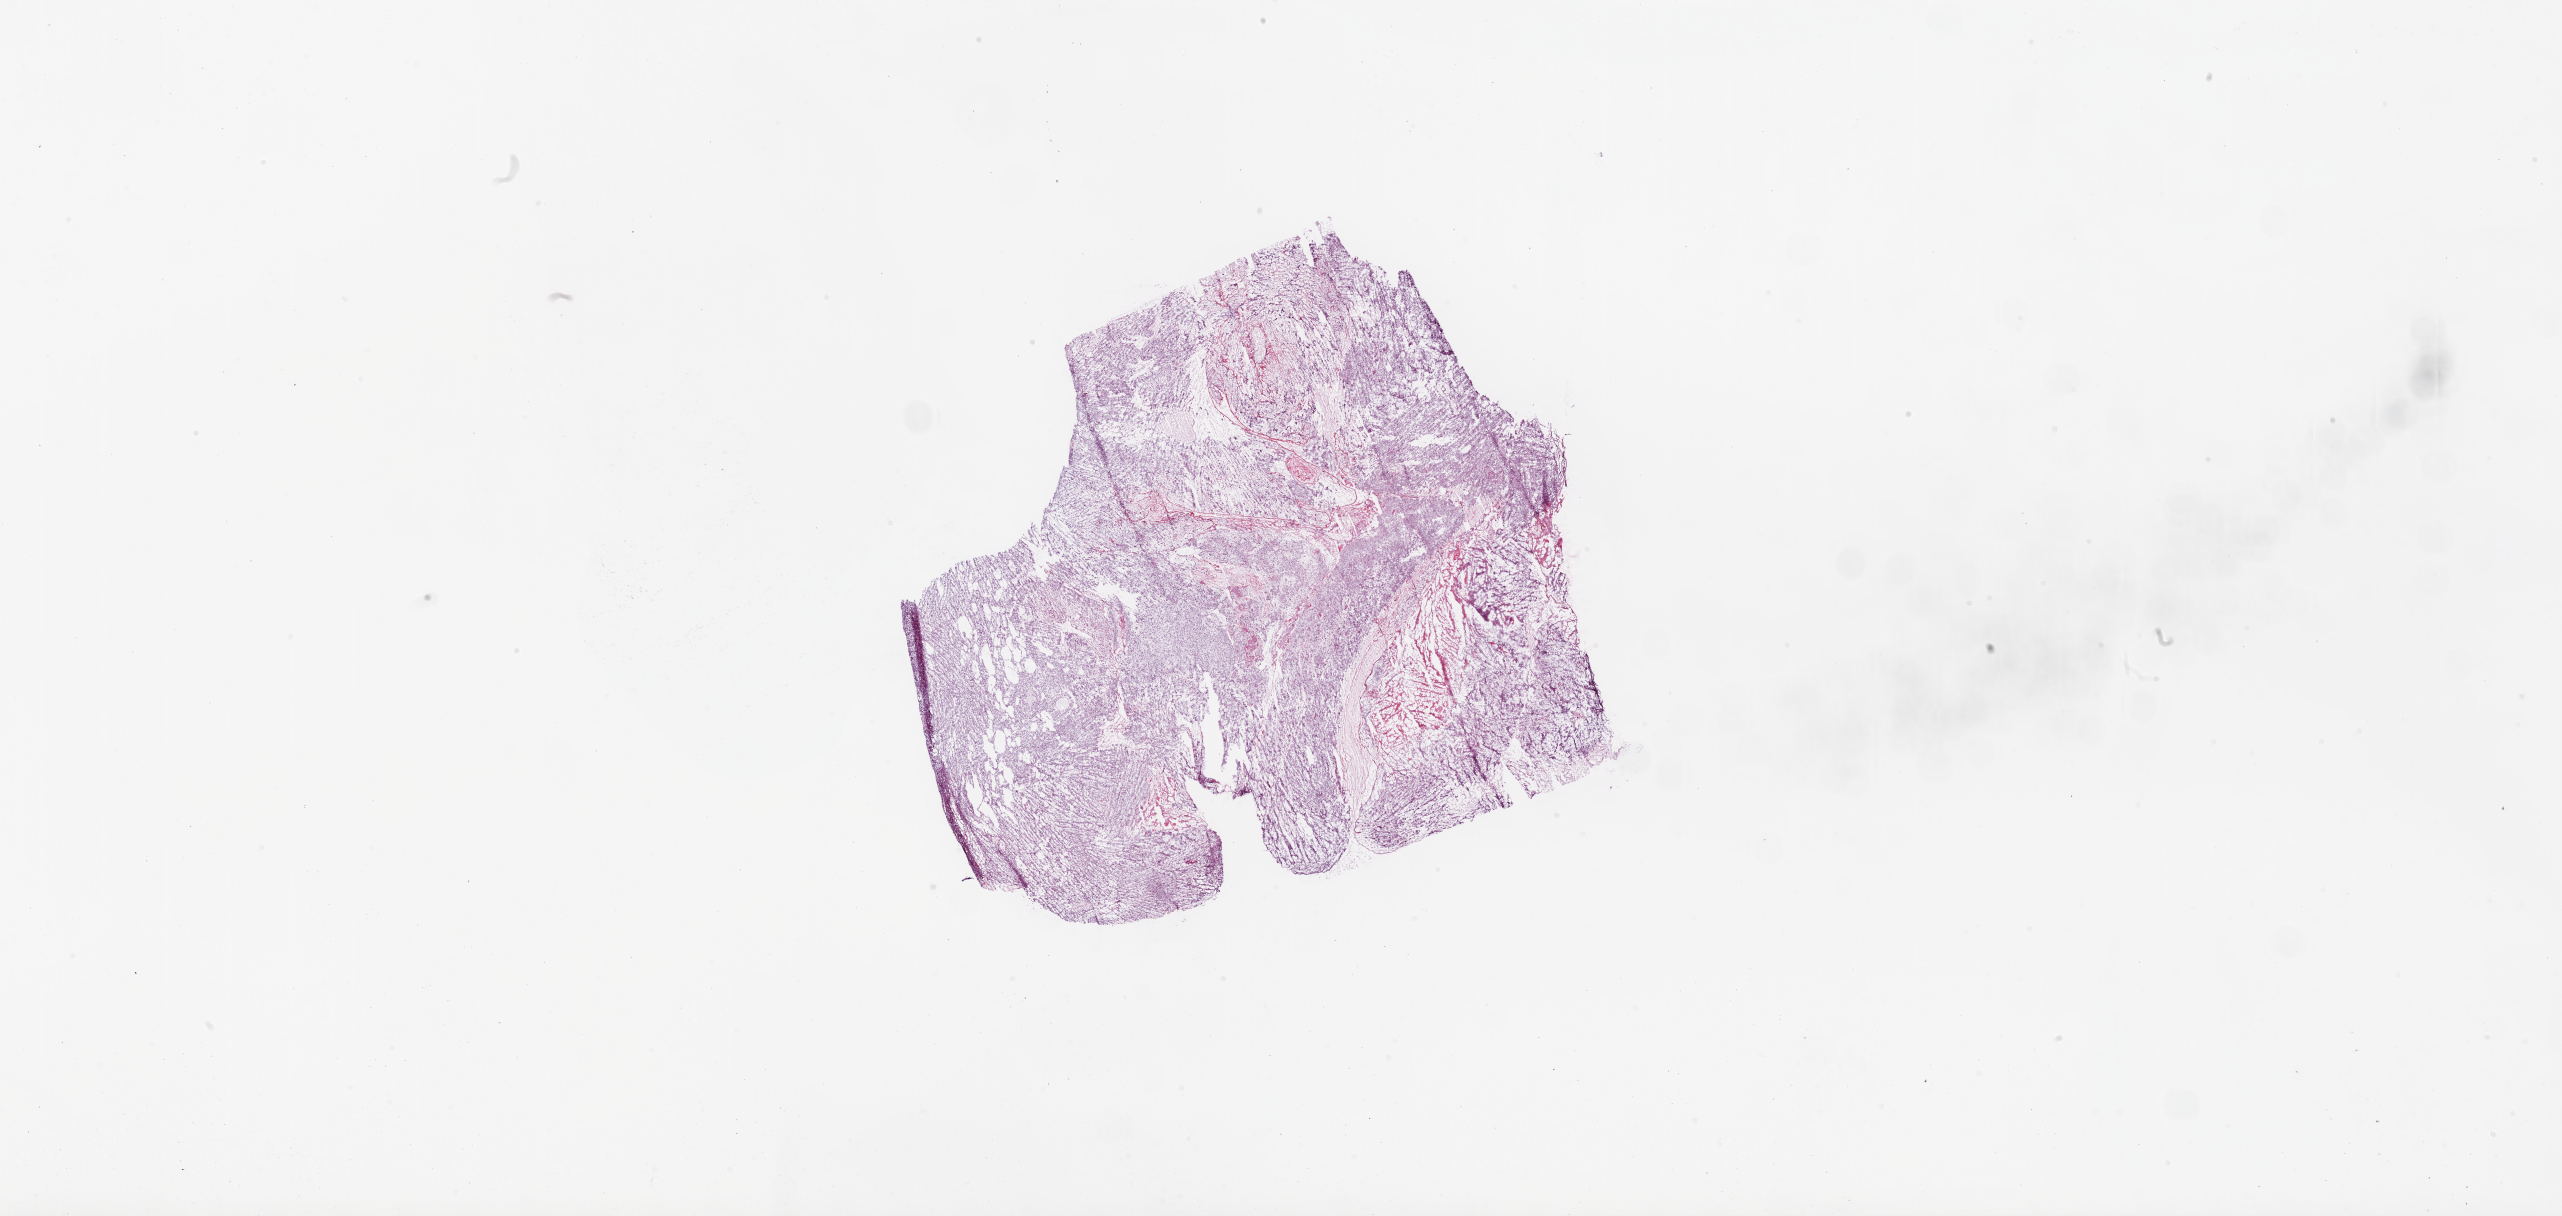
Whole-slide histology image, H&E-stained — whole scanned area (about 41.1 x 19.5 mm) shown as a low-resolution overview; frozen section from the bottom of the tissue portion; primary tumour sample from the brain. Male, age 65 years at initial diagnosis. Pathologist review of this section (percent, as recorded): tumour cells 80%, tumour nuclei 80%, normal cells 0%, stromal cells 0%, necrosis 20%.
Diagnosis: Glioblastoma.